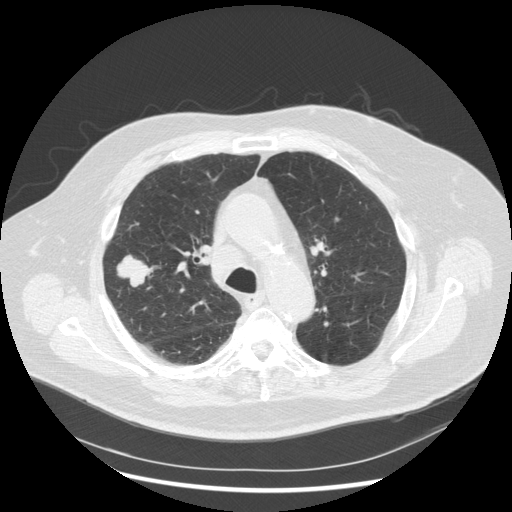
Low-dose screening chest CT, axial slice; third annual screen; lung window (W 1500 / L -600 HU); 2.5 mm slice thickness; standard (soft-tissue) reconstruction kernel (STANDARD); slice 192 of 263 in the series; 512 × 512 image matrix, field of view 400 × 400 mm. Male, age 72 years at enrolment. Former smoker at enrolment.
Expert reader's lesion annotation, bounding box [x1, y1, x2, y2] px = [102, 250, 158, 298]. Reader record for this screening exam (exam-level; its link to the box is not recorded): non-calcified nodule or mass ≥4 mm, right upper lobe, 31 × 31 mm, poorly defined margins, soft tissue attenuation, pre-existing on the prior screen: no. Official screen result: positive, other. Later outcome: lung cancer diagnosed 70 days after this screen — squamous cell carcinoma, NOS, right upper lobe, poorly differentiated (G3), stage IIIA (AJCC 6th edition), 19 mm at pathology.